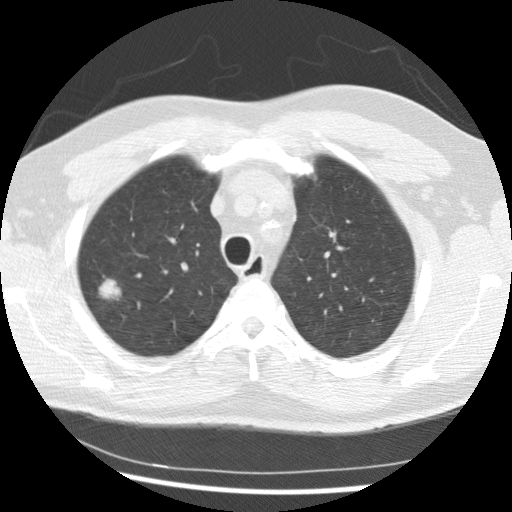
Chest CT (low-dose screening protocol), one axial image. First (baseline) screen. Lung window (W 1500 / L -600 HU). 2.5 mm slice thickness. Standard (soft-tissue) reconstruction kernel (STANDARD). Male, age 56 years at enrolment. Current smoker at enrolment.
- Lesion marked by an expert reader, bounding box [x1, y1, x2, y2] px = [77, 268, 131, 315].
- Screening reader's record for this exam (one nodule recorded; not confirmed to be the boxed lesion): non-calcified nodule or mass ≥4 mm, right upper lobe, 19 × 15 mm, spiculated (stellate) margins, soft tissue attenuation.
- Official screen result: positive, change unspecified: nodule(s) >= 4 mm or enlarging nodule(s), mass(es), or other non-specific abnormalities suspicious for lung cancer.
- Later outcome: lung cancer diagnosed 291 days after this screen — non-small cell carcinoma, right upper lobe, poorly differentiated (G3), stage IIIB (AJCC 6th edition), 20 mm at pathology.